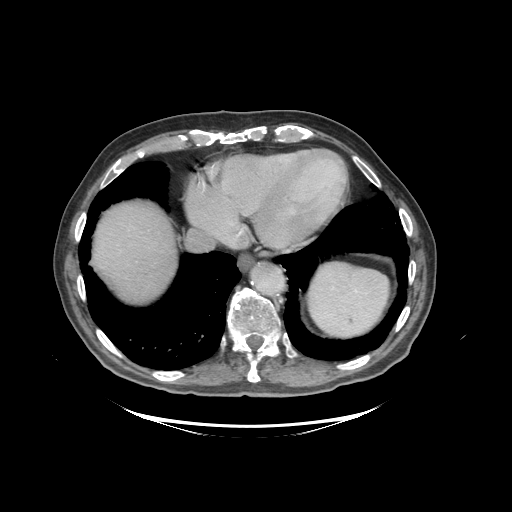
Contrast-enhanced abdominal CT (liver protocol), one axial slice. Position 87 of 99 along the scan axis. Soft-tissue window (W 400 / L 40 HU). 2.5 mm slice thickness. 512 × 512 image matrix, field of view 460 × 460 mm. Case-level facts recorded for this patient, not image findings: diagnosis: hepatocellular carcinoma (patient treated with transarterial chemoembolisation; whether this scan precedes or follows treatment is not stated here); TNM stage (as recorded): Stage-I.
Structures marked on this image (semi-automatic segmentation, software-assisted and operator-edited):
- abdominal aorta: bounding box [x1, y1, x2, y2] px = [254, 264, 285, 294]
- liver parenchyma outside the tumour (the mass and vessels are separate outlines, so this box may not span the whole liver): [92, 202, 176, 300]